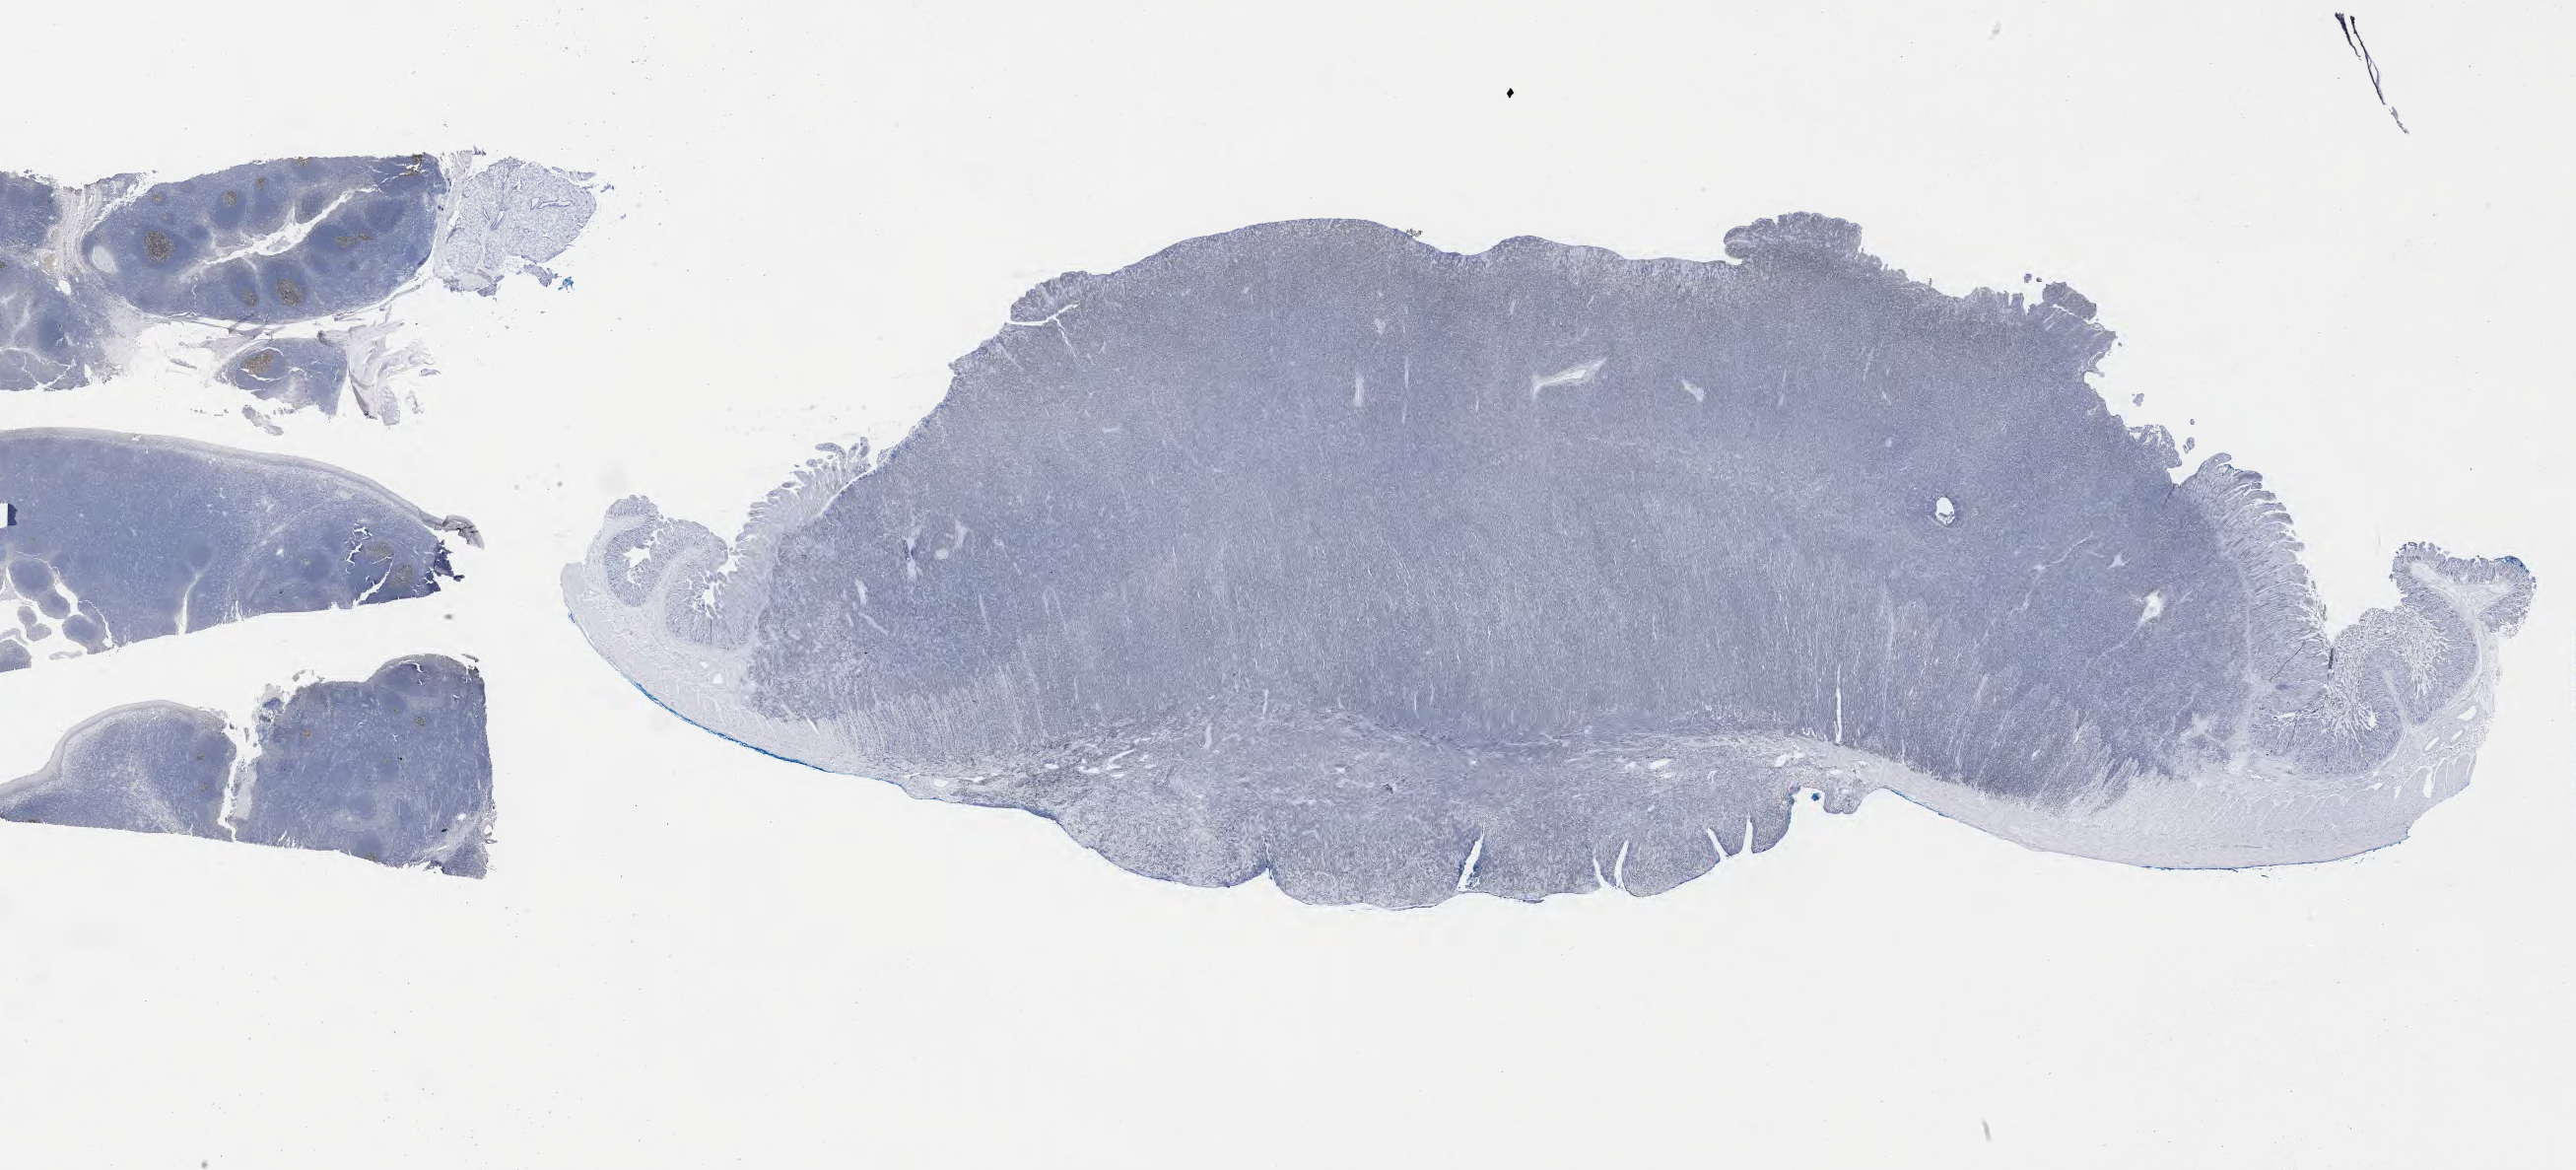
Whole-slide image, immunohistochemical stain for BCL6 — whole scanned area (about 42.3 x 19.2 mm) shown as a low-resolution overview, specimen: tumor tissue, anatomic site: small intestine. Patient: male, age at initial diagnosis 6 years.
Diagnosis: Burkitt lymphoma, NOS.